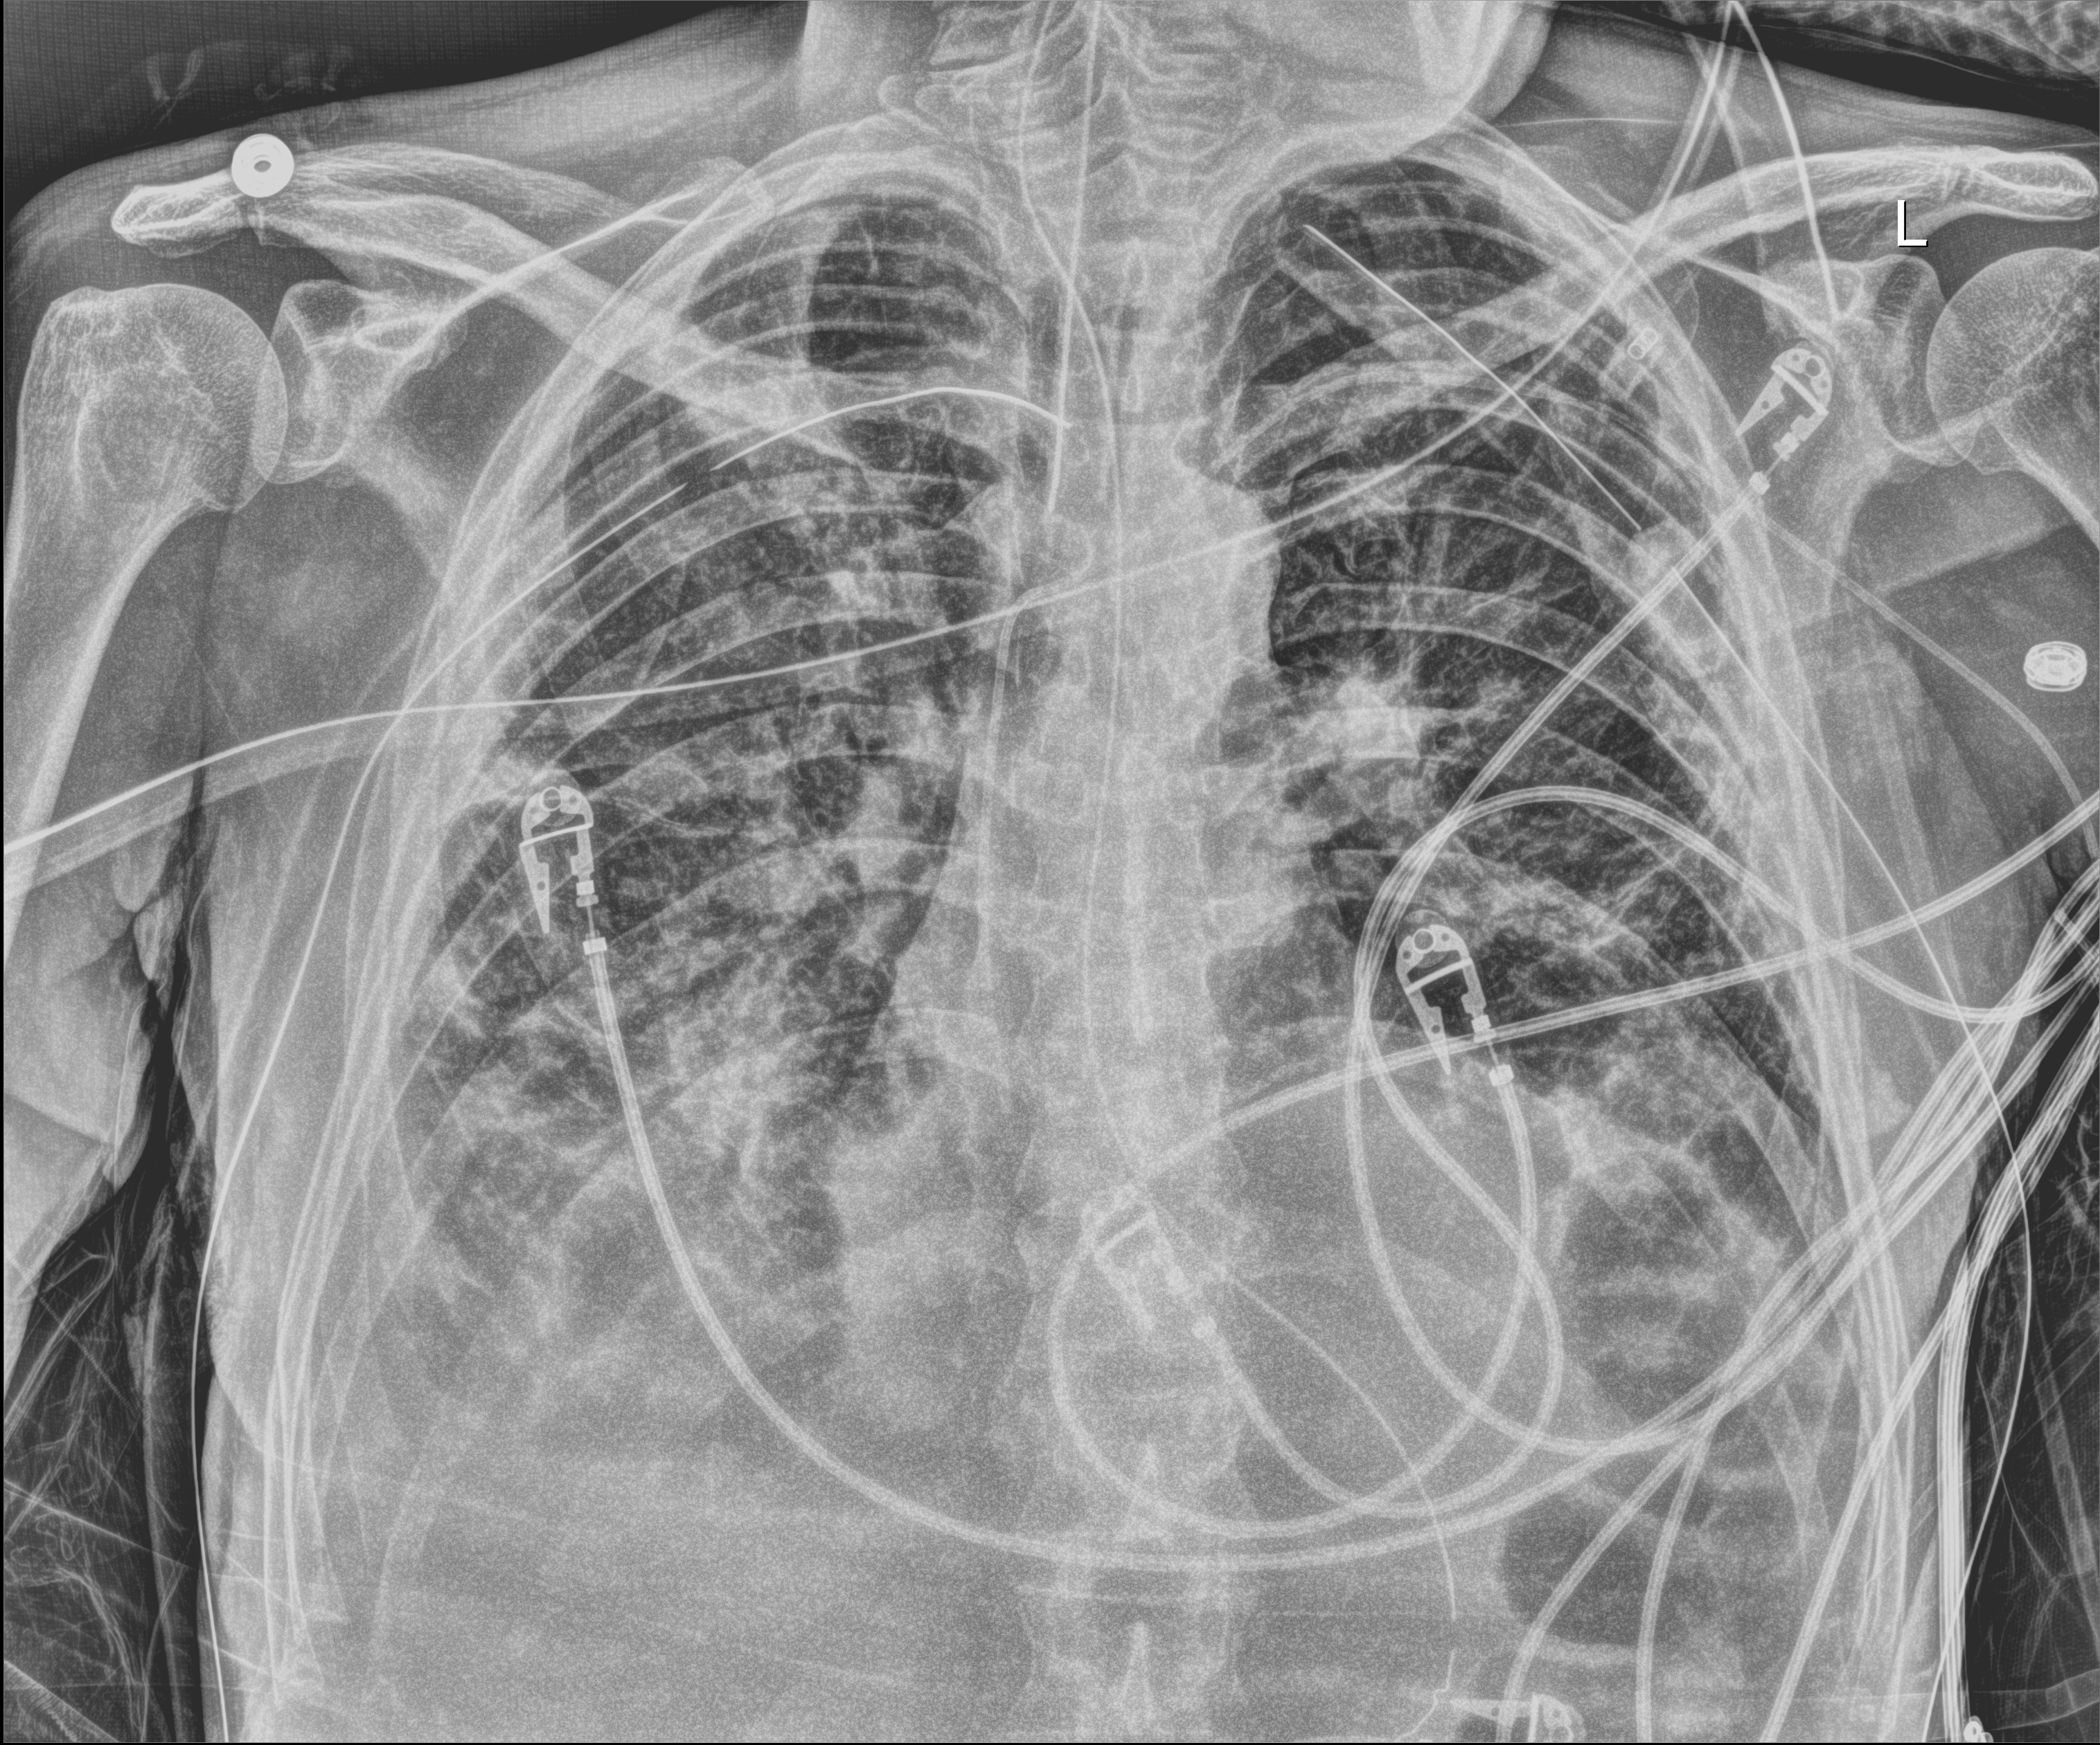
Chest radiograph, anteroposterior (AP) projection. Male patient hospitalised with COVID-19, age 18–59 years.
From the hospital-stay record, not from the radiograph (when in the stay this image was taken is not recorded):
- mechanically ventilated during this hospital stay: yes
- COPD (admission record): no
- admitted to intensive care during this hospital stay: yes